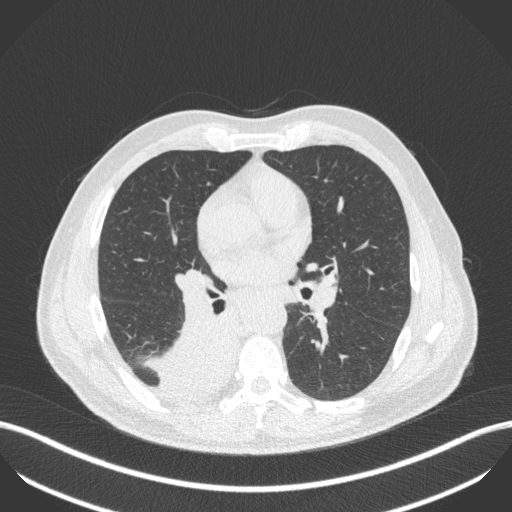
Chest CT, one axial slice; position 252 of 451 along the scan axis; reconstruction kernel B31f; lung window (W 1500 / L -600 HU); 1 mm slice thickness; 512 × 512 image matrix. Patient: male, 61 years. Case-level facts recorded for this patient, not image findings: clinical TNM (as recorded): T1 N0 M0.
Annotated regions visible in this slice (rectangle marked by the reading radiologist):
- lung tumour (recorded histology: small cell carcinoma): bounding box (x1, y1, x2, y2) in pixels: (149, 308, 238, 403)